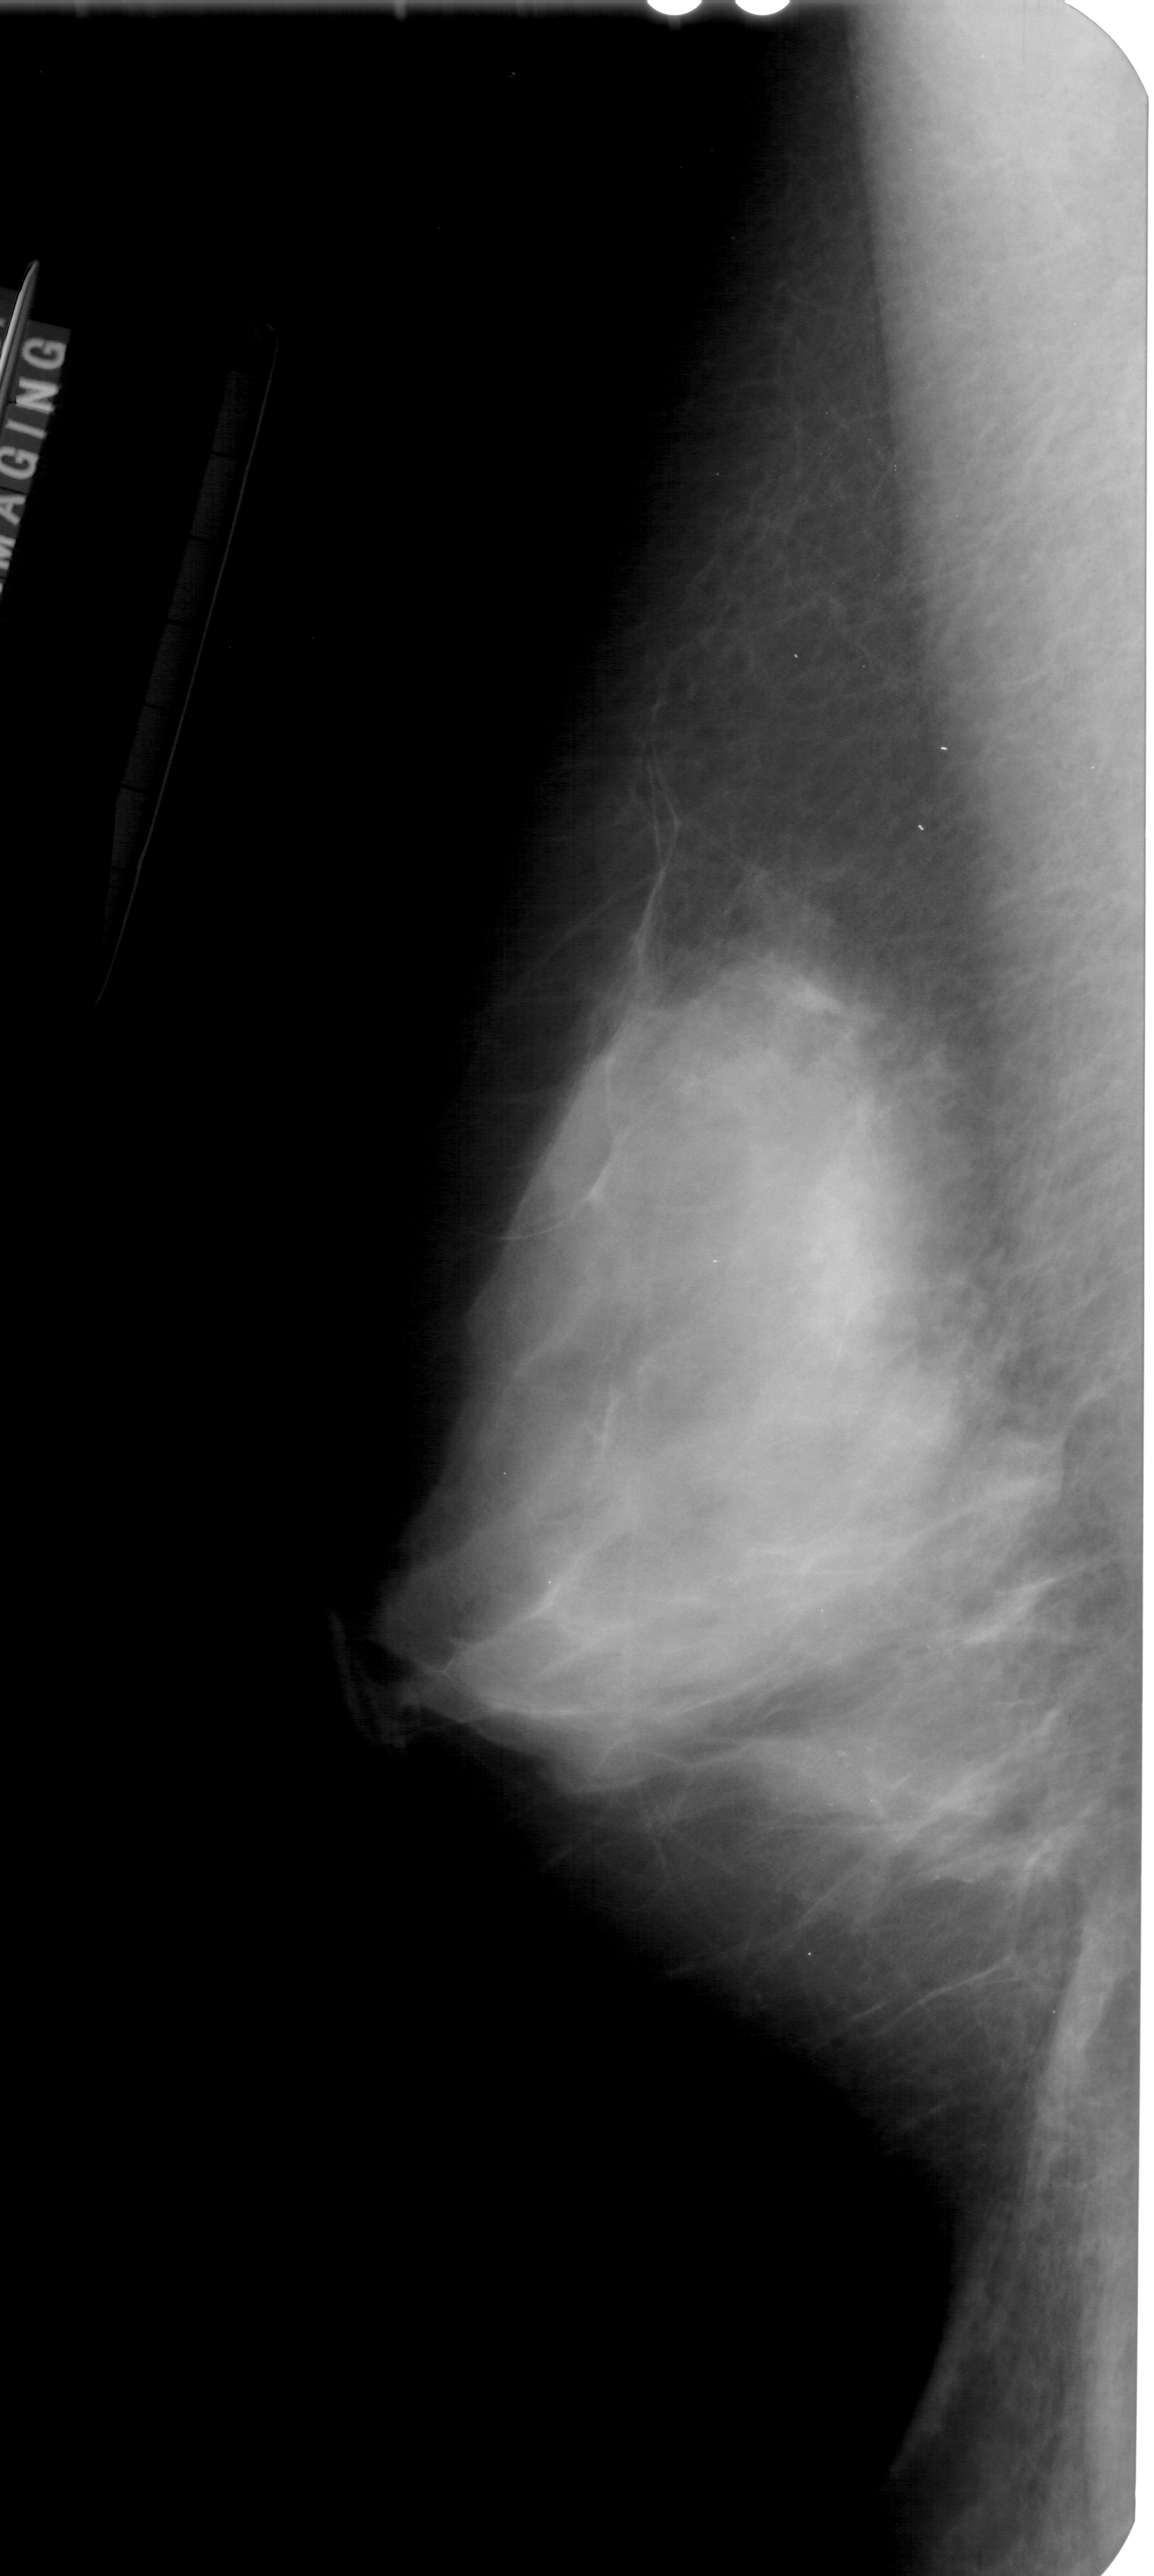
Scanned film-screen mammogram; left breast; MLO view; breast composition: extremely dense (BI-RADS density category 4 of 4).
- Calcifications, morphology pleomorphic, distribution clustered; BI-RADS assessment category 4; subtlety rating 2 on a 1 (subtle) to 5 (obvious) scale; pathology result (as recorded, not read from the image): benign.